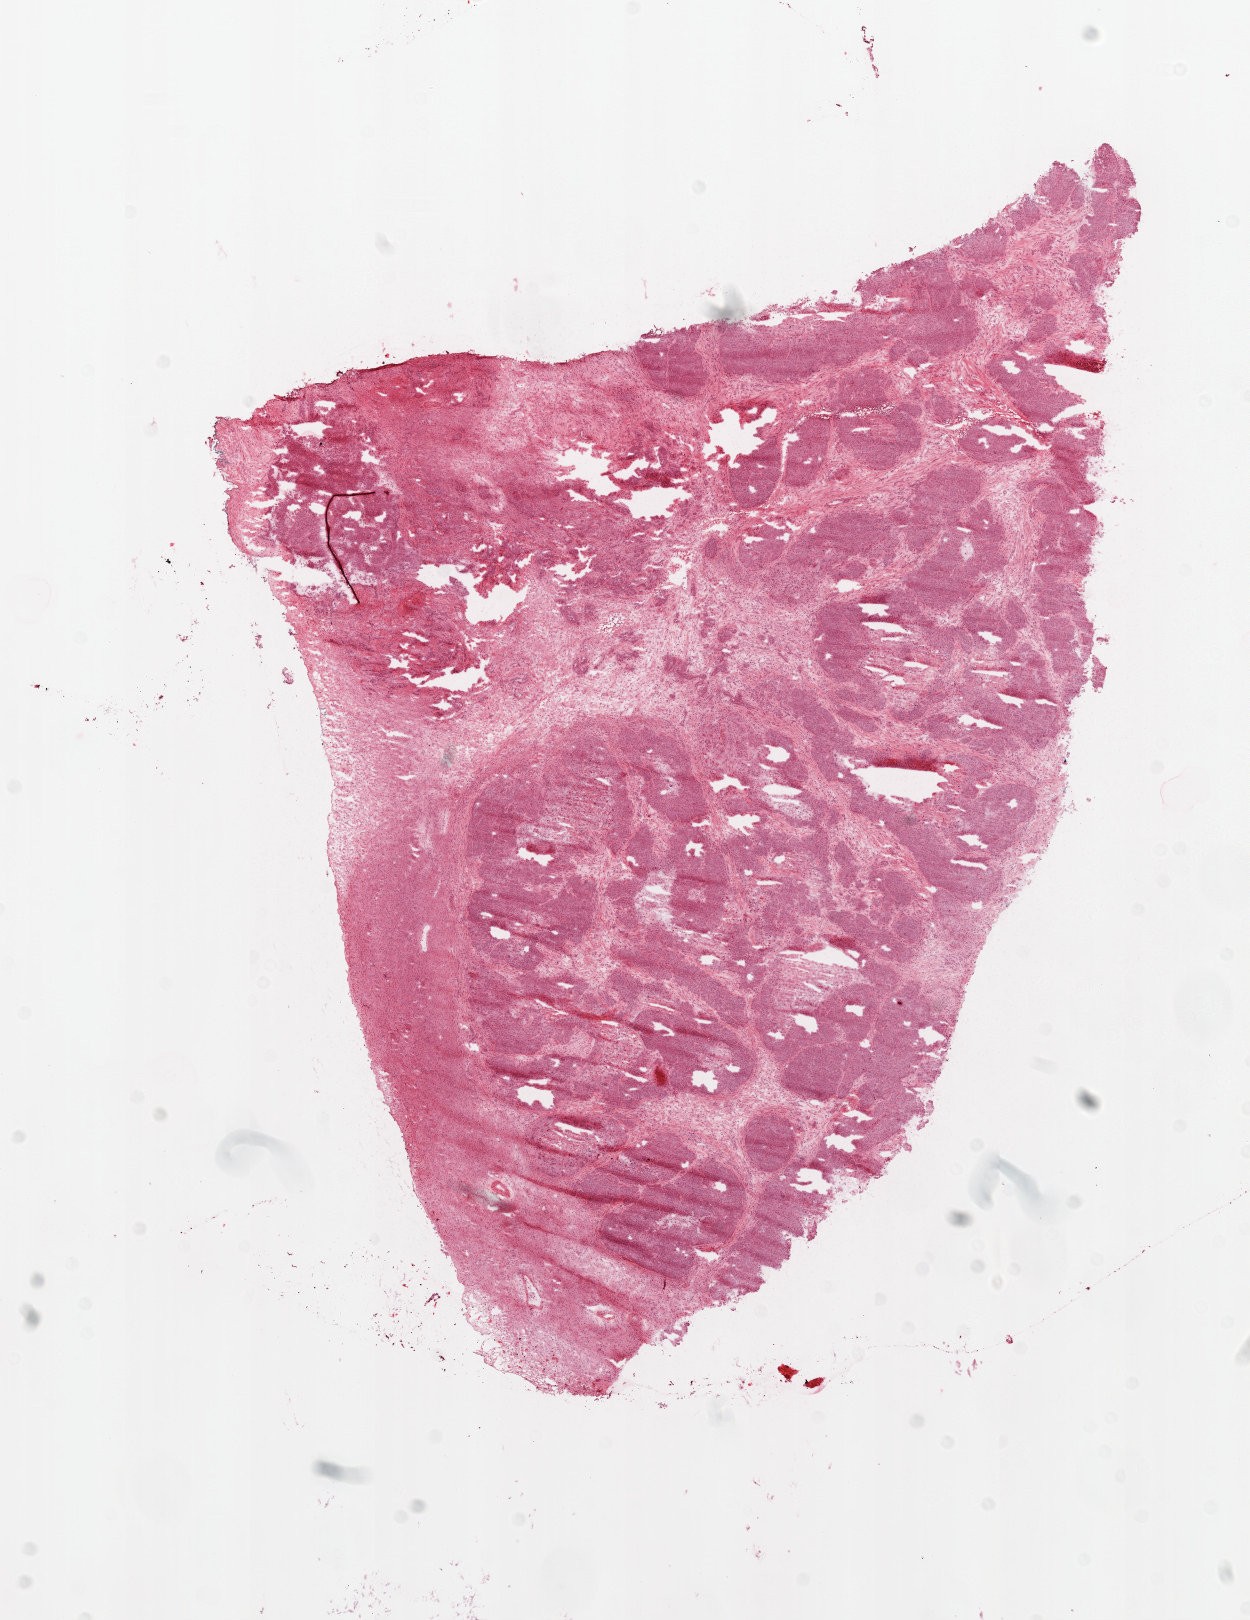
H&E whole-slide image — shown as a low-resolution overview of the whole scanned area (about 10.0 x 13.0 mm). Frozen section from the top of the tissue portion. Sample: primary tumour, ovary. Female patient; age at initial diagnosis 47 years. Histologic grade: G3 (poorly differentiated). Pathologist review of this section (percent, as recorded): tumour cells 70%, tumour nuclei 90%, normal cells 0%, stromal cells 20%, necrosis 5%.
- FIGO stage: IIIC
- histologic diagnosis: Serous cystadenocarcinoma, NOS